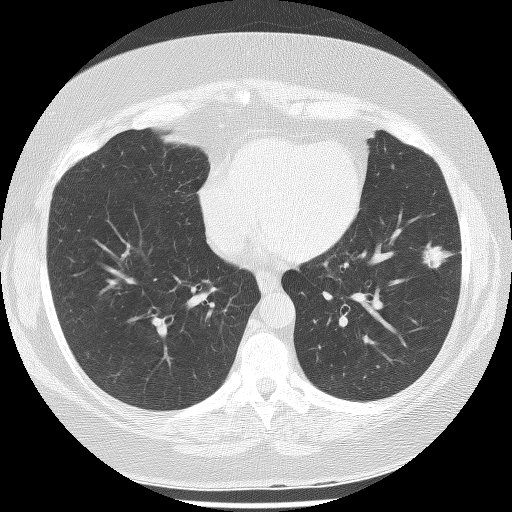
Chest CT (low-dose screening protocol), one axial image, first (baseline) screen, lung window (W 1500 / L -600 HU). Female participant, aged 56 years at enrolment.
• Lesion marked by an expert reader, bounding box <392,225,464,284> (left, top, right, bottom; pixels).
• Screening reader's record for this exam (one nodule recorded; not confirmed to be the boxed lesion): non-calcified nodule or mass ≥4 mm, left lower lobe, 22 × 17 mm, spiculated (stellate) margins, soft tissue attenuation.
• Official screen result: positive, change unspecified: nodule(s) >= 4 mm or enlarging nodule(s), mass(es), or other non-specific abnormalities suspicious for lung cancer.
• Lung cancer was diagnosed 63 days after this screen: bronchiolo-alveolar adenocarcinoma, NOS, left lower lobe, stage IA (AJCC 6th edition), 18 mm at pathology.